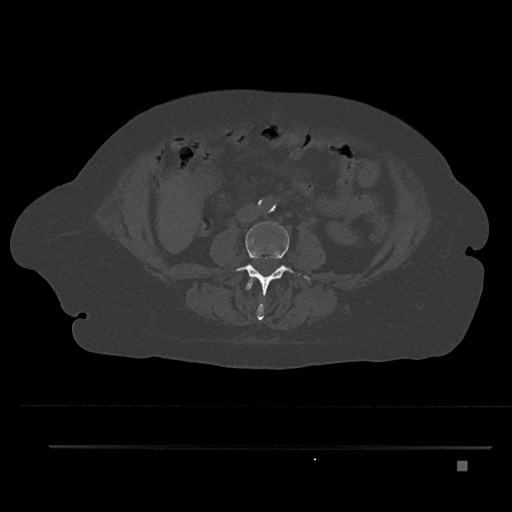
CT including the spine, one axial slice. Slice 127 of 797 in the series (ordered by position). 120 kVp. Bone window (W 1800 / L 400 HU). 512 × 512 image matrix. Patient: female, 76 years. Case-level facts recorded for this patient, not image findings: primary cancer: lung; vertebrae with lytic lesions (as recorded): T11, L3.
Annotated regions visible in this slice (semi-automatically segmented with operator editing):
- L2 vertebra: box from (x=246, y=278) to (x=264, y=321) px
- L3 vertebra: (x=232, y=222)–(x=311, y=296)